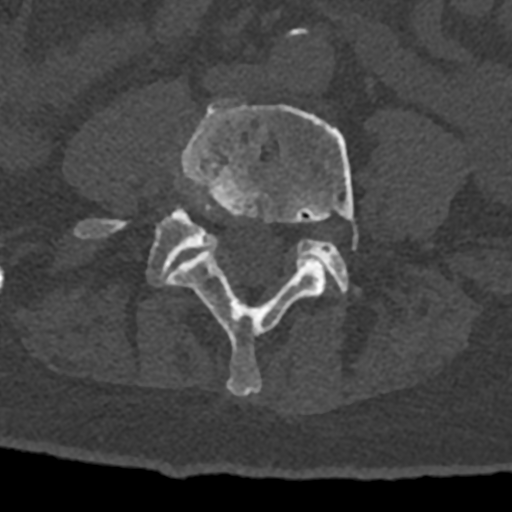
CT including the spine, one axial slice; 120 kVp; bone window (W 1800 / L 400 HU); 0.5 mm slice thickness; 512 × 512 image matrix. Patient: male, 74 years. Case-level facts recorded for this patient, not image findings: primary cancer: renal.
Structures marked on this image (semi-automatically segmented with operator editing):
- L4 vertebra: bounding box [x1, y1, x2, y2] px = [167, 99, 358, 396]
- L5 vertebra: [75, 209, 349, 293]